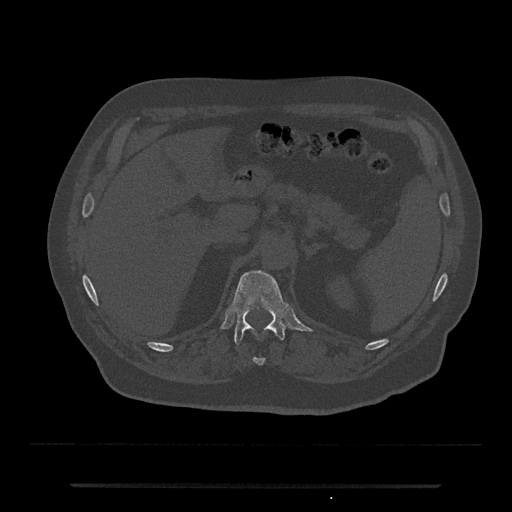
CT including the spine, one axial slice. Slice 604 of 797 in the series (ordered by position). Reconstruction kernel Br40s/3. 120 kVp. Bone window (W 1800 / L 400 HU). 0.5 mm slice thickness. 512 × 512 image matrix, field of view 434 × 434 mm. Patient: male, 80 years. From the clinical record (not read from this slice): primary cancer: prostate; vertebrae with lytic lesions (as recorded): L1, T11.
Structures marked on this image (semi-automatic segmentation, software-assisted and operator-edited):
- T11 vertebra: bounding box (x1, y1, x2, y2) in pixels: (253, 357, 265, 365)
- T12 vertebra: (229, 270, 289, 345)